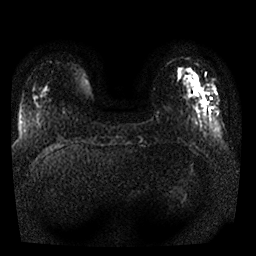
Breast MRI, one axial slice. Slice 4 of 25 in the series (ordered by position). Diffusion-weighted series; image 2 of 4 stored at this slice position (different b-values; order by instance number). 1.5 T. 256 × 256 image matrix, field of view 330 × 330 mm. Female patient.
Outlined on this slice (manually delineated by an expert):
- tumour on diffusion-weighted imaging: box from (x=203, y=100) to (x=207, y=104) px